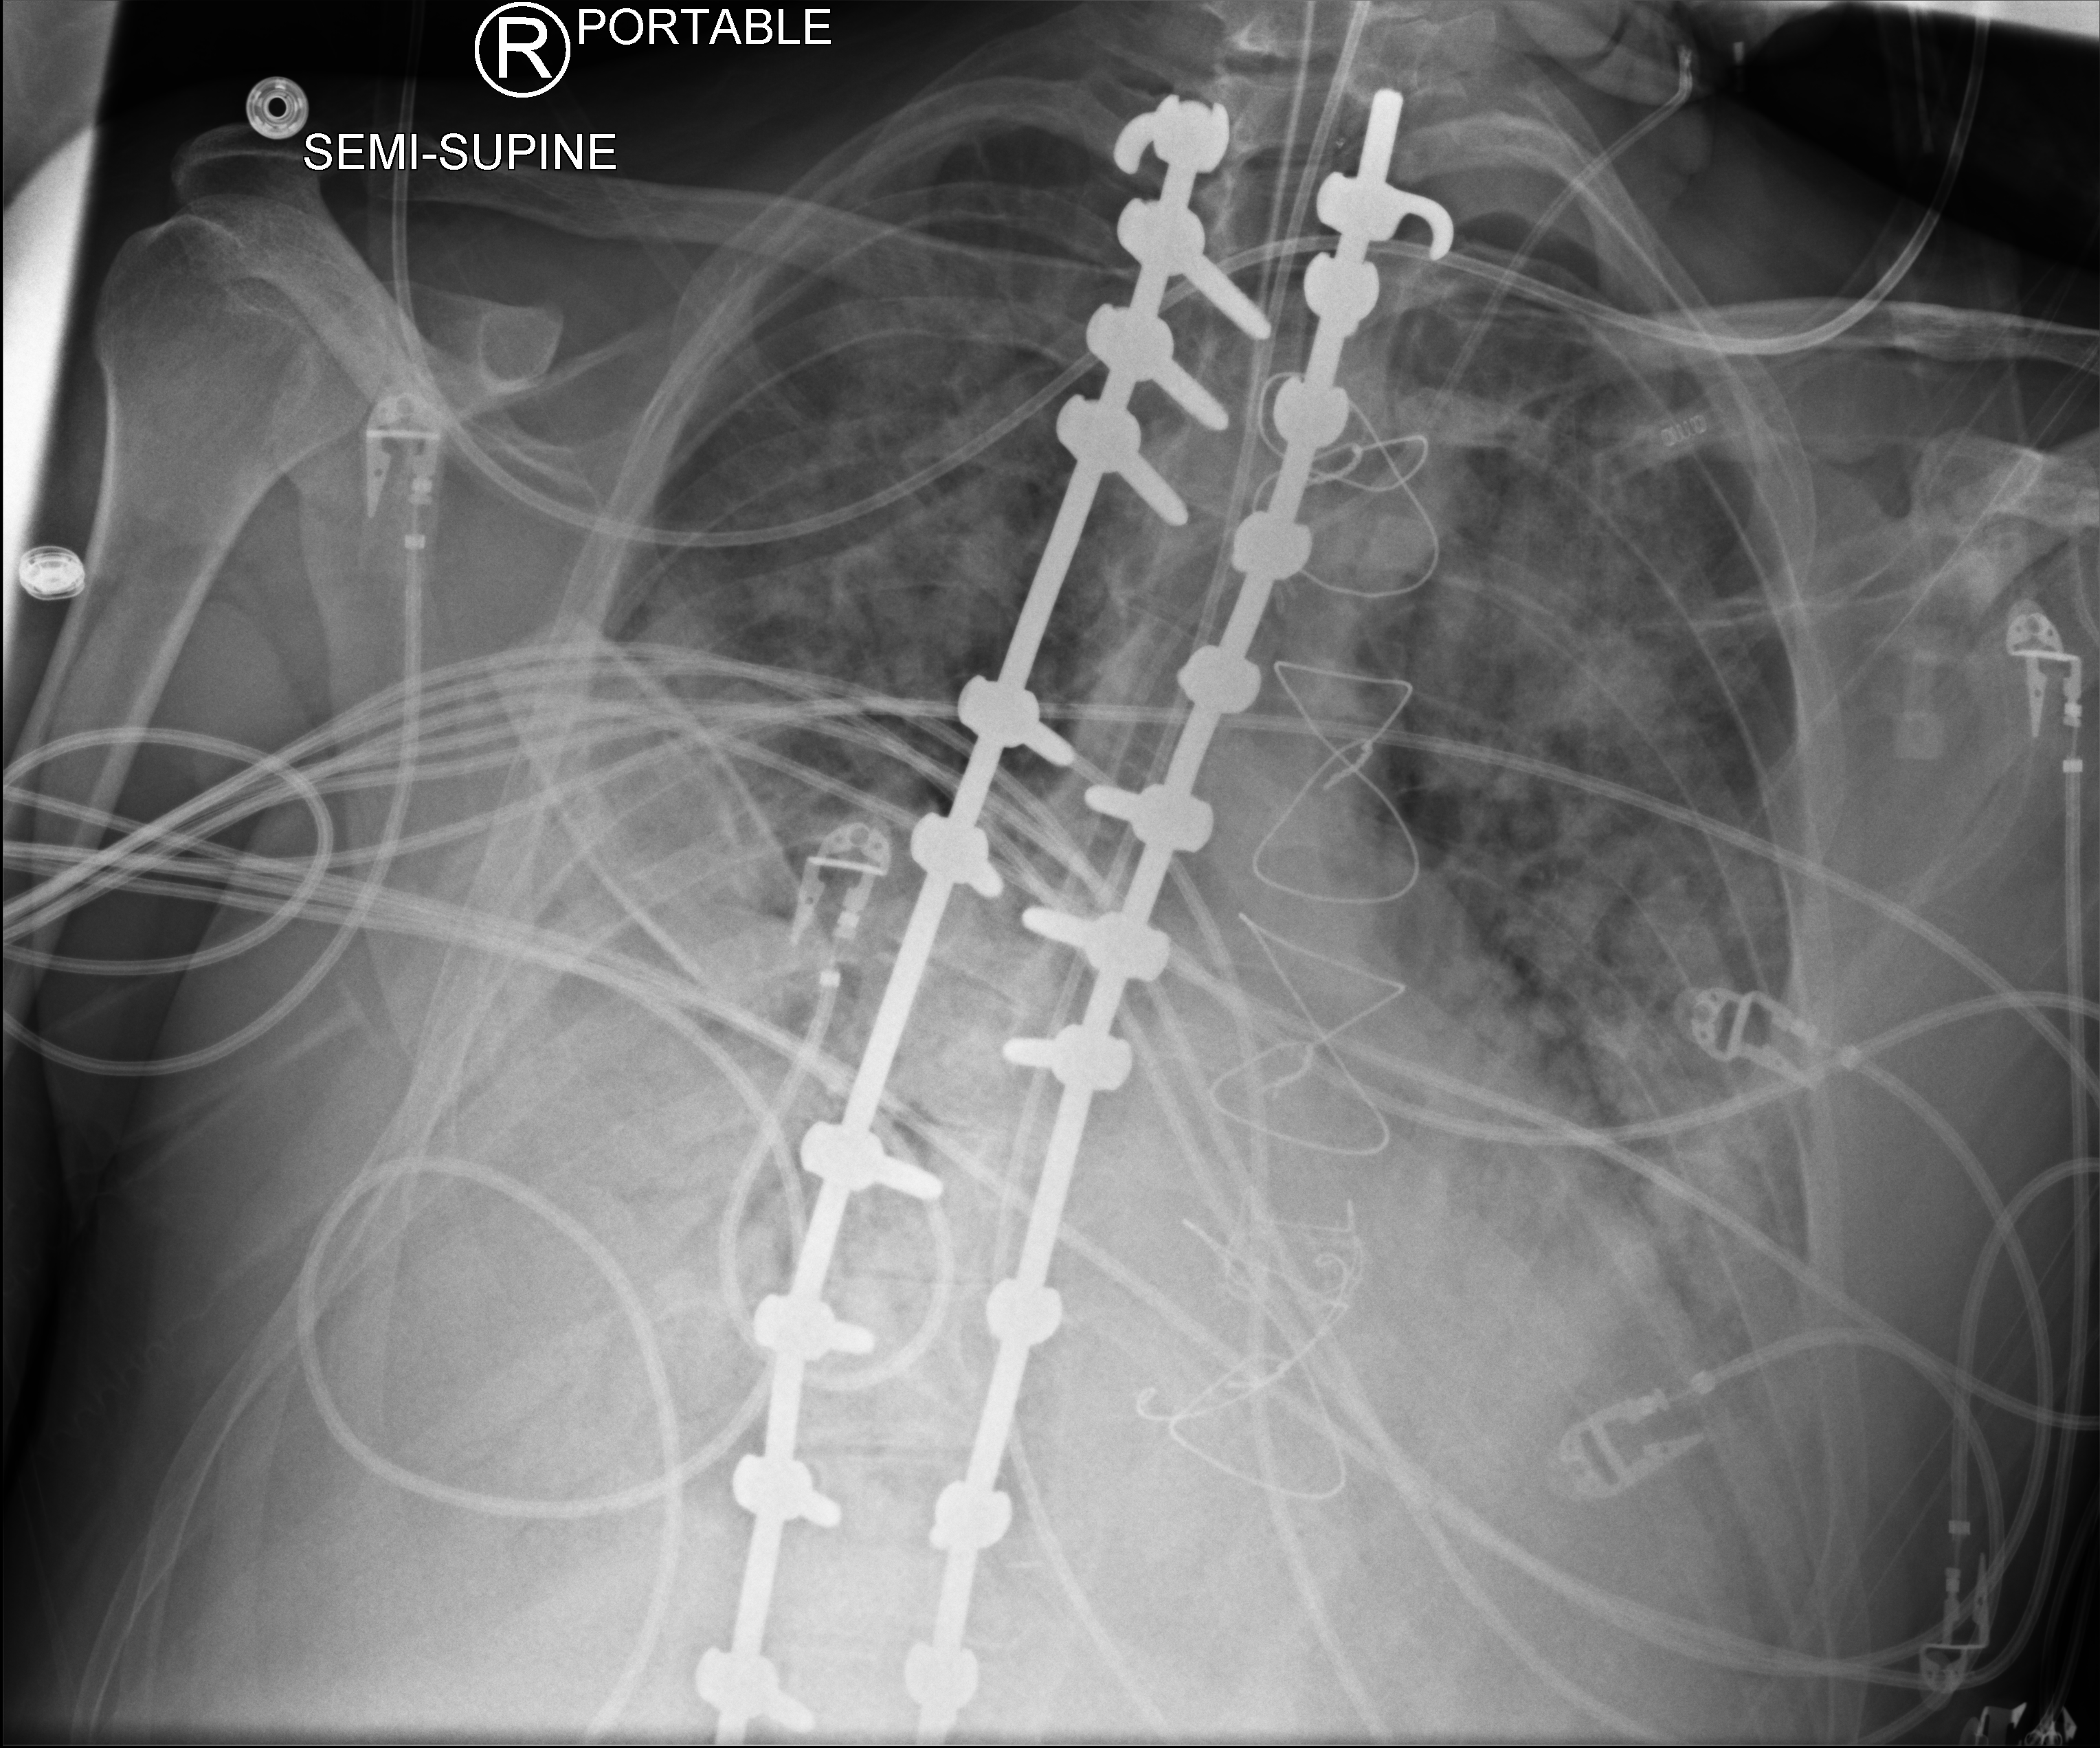
Chest X-ray (portable); anteroposterior (AP) projection. Adult patient hospitalised with COVID-19, age 18–59 years.
From the hospital-stay record, not from the radiograph (when in the stay this image was taken is not recorded):
- admitted to intensive care during this hospital stay: yes
- chronic kidney disease (admission record): no